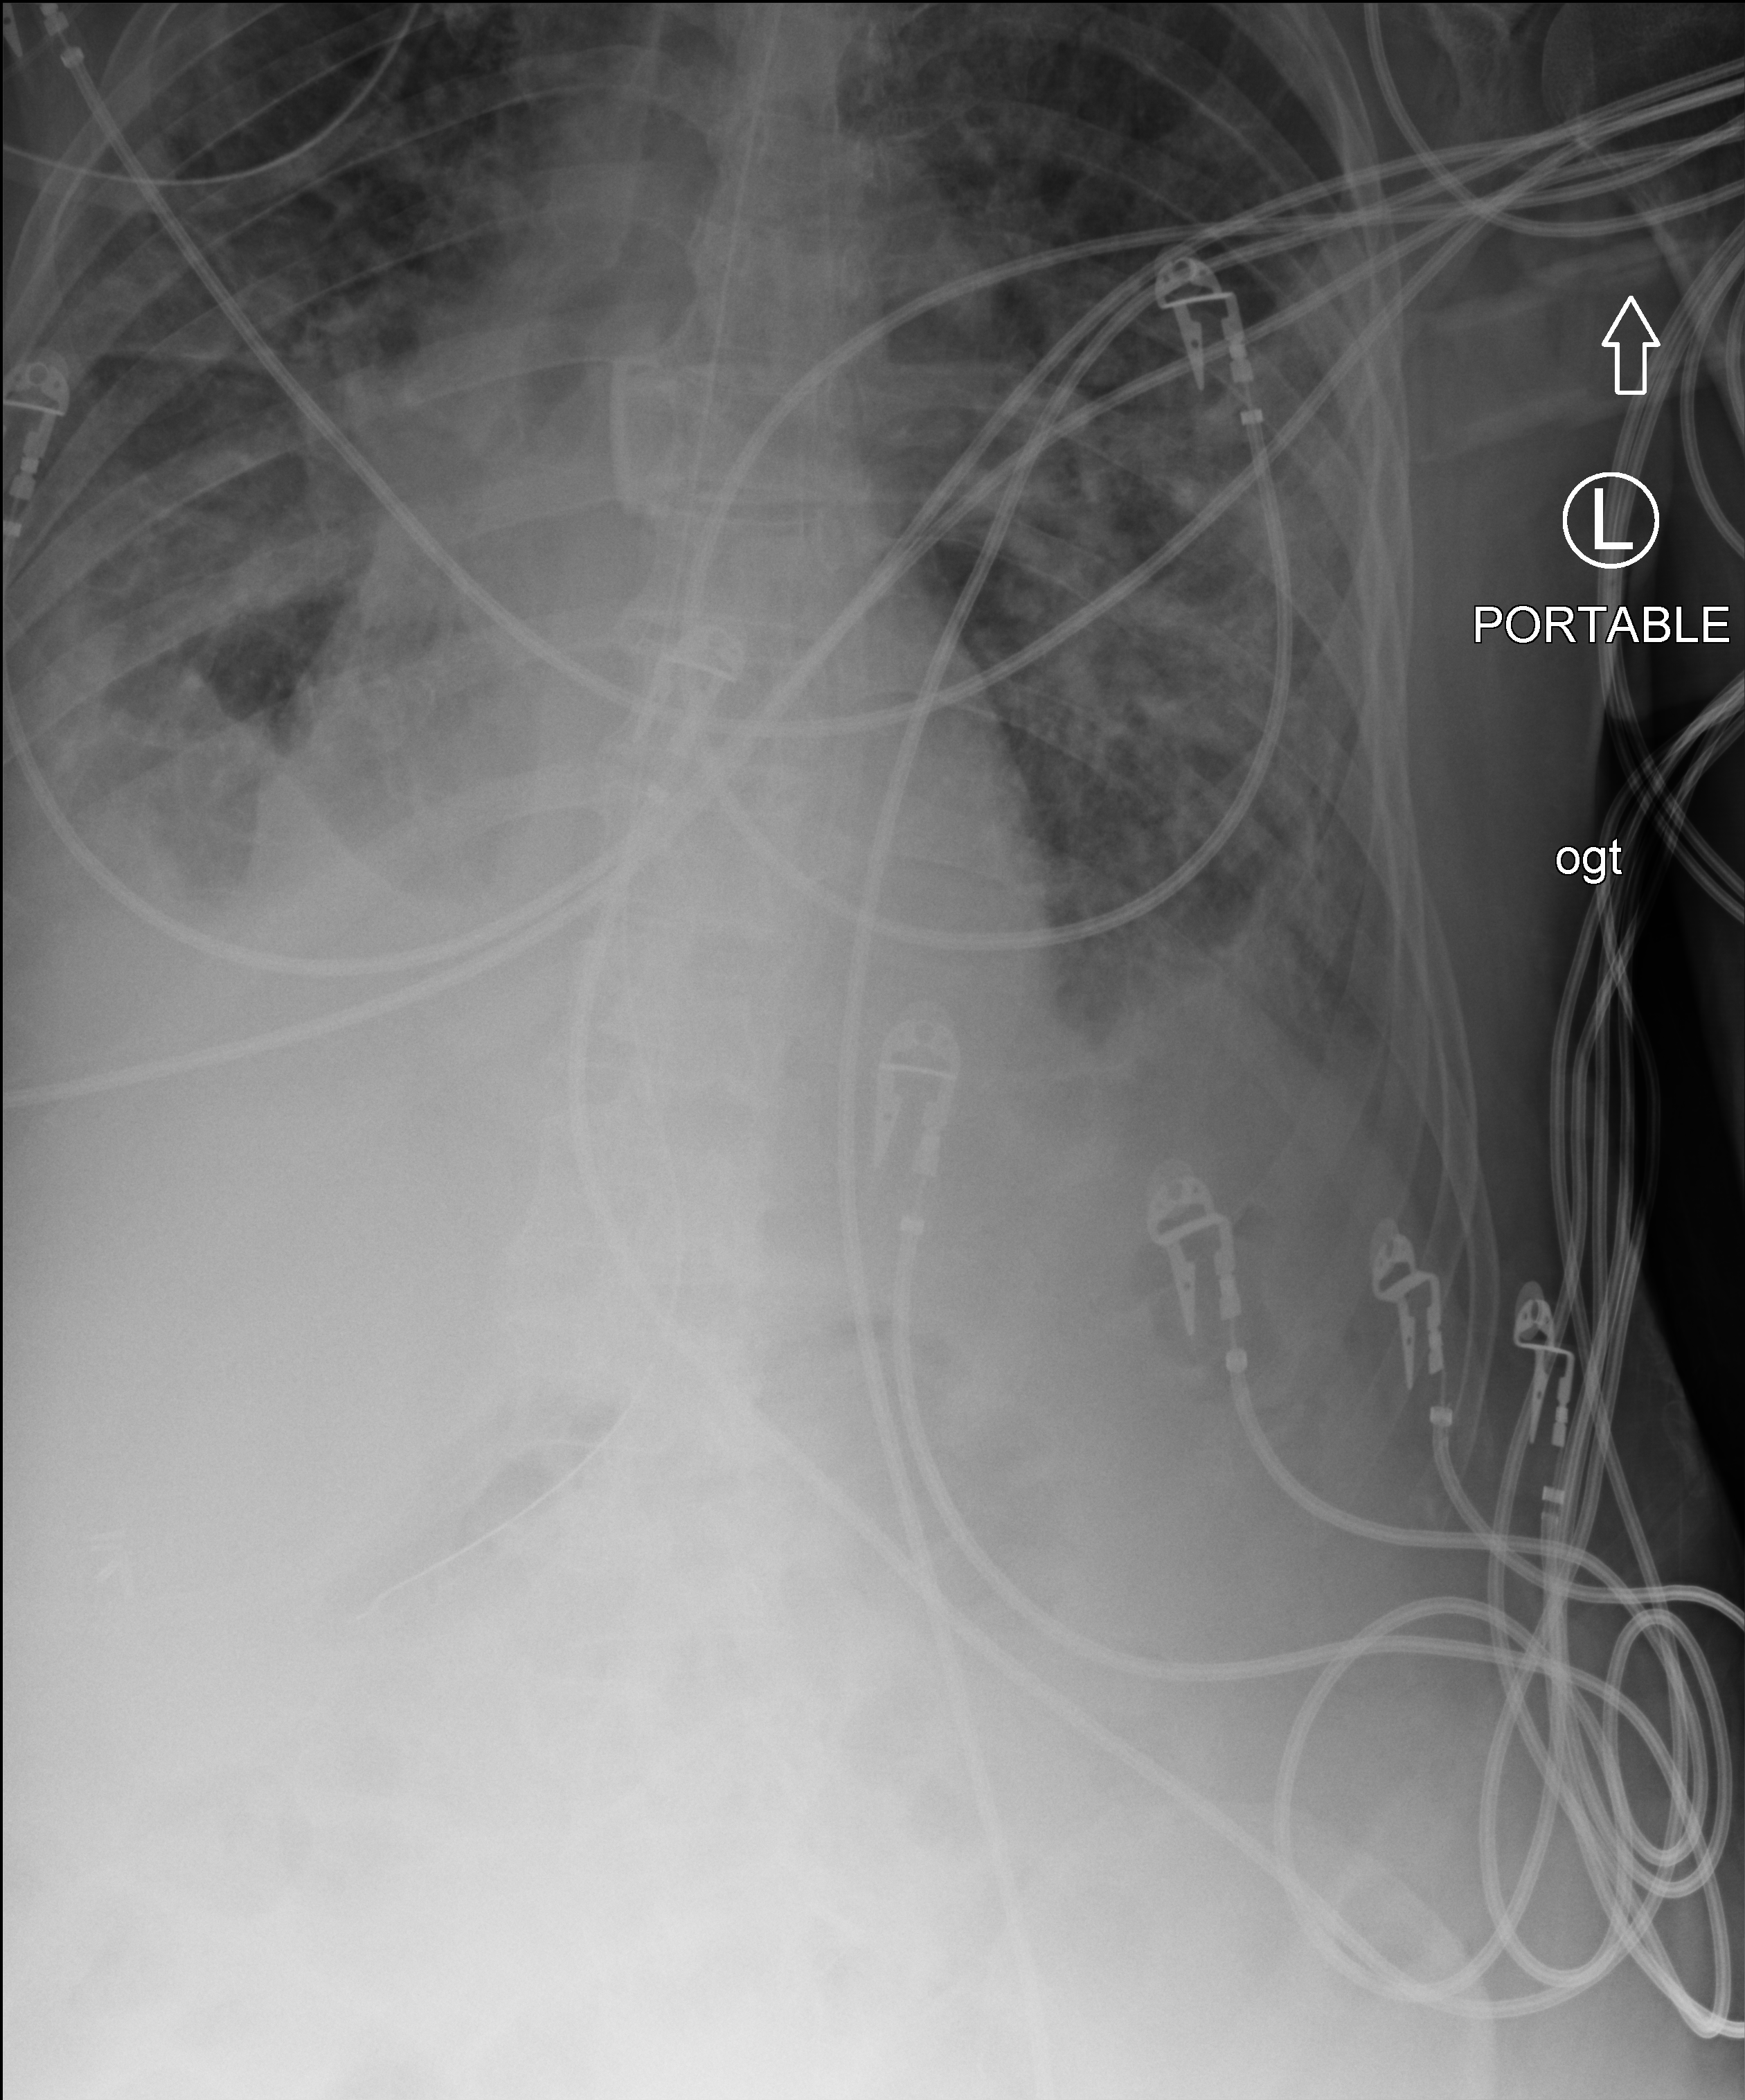
Bedside chest radiograph (computed radiography); anteroposterior (AP) projection. Male patient hospitalised with COVID-19, age 75–90 years.
From the hospital-stay record, not from the radiograph (when in the stay this image was taken is not recorded):
- mechanically ventilated during this hospital stay: yes